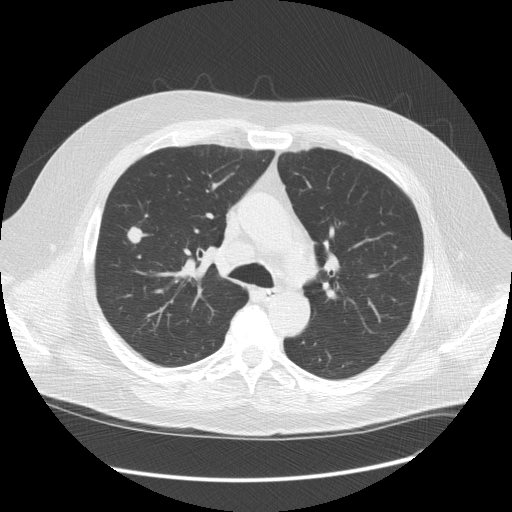
Chest CT (low-dose screening protocol), one axial image; third annual screen; lung window (W 1500 / L -600 HU); 512 × 512 image matrix, field of view 401 × 401 mm. Male participant, aged 61 years at enrolment. Current smoker at enrolment.
Expert reader's lesion annotation, box from (x=108, y=218) to (x=151, y=257) px. The exam's reader record, not a measurement of the box and not confirmed to be the same lesion: non-calcified nodule or mass ≥4 mm, right upper lobe, 13 × 11 mm, spiculated (stellate) margins, soft tissue attenuation, pre-existing on the prior screen: yes; interval growth: yes. Official screen result: positive, other. Participant outcome: lung cancer diagnosed 21 days after this screen — adenocarcinoma, NOS, right upper lobe, stage IIIA (AJCC 6th edition), 13 mm at pathology.